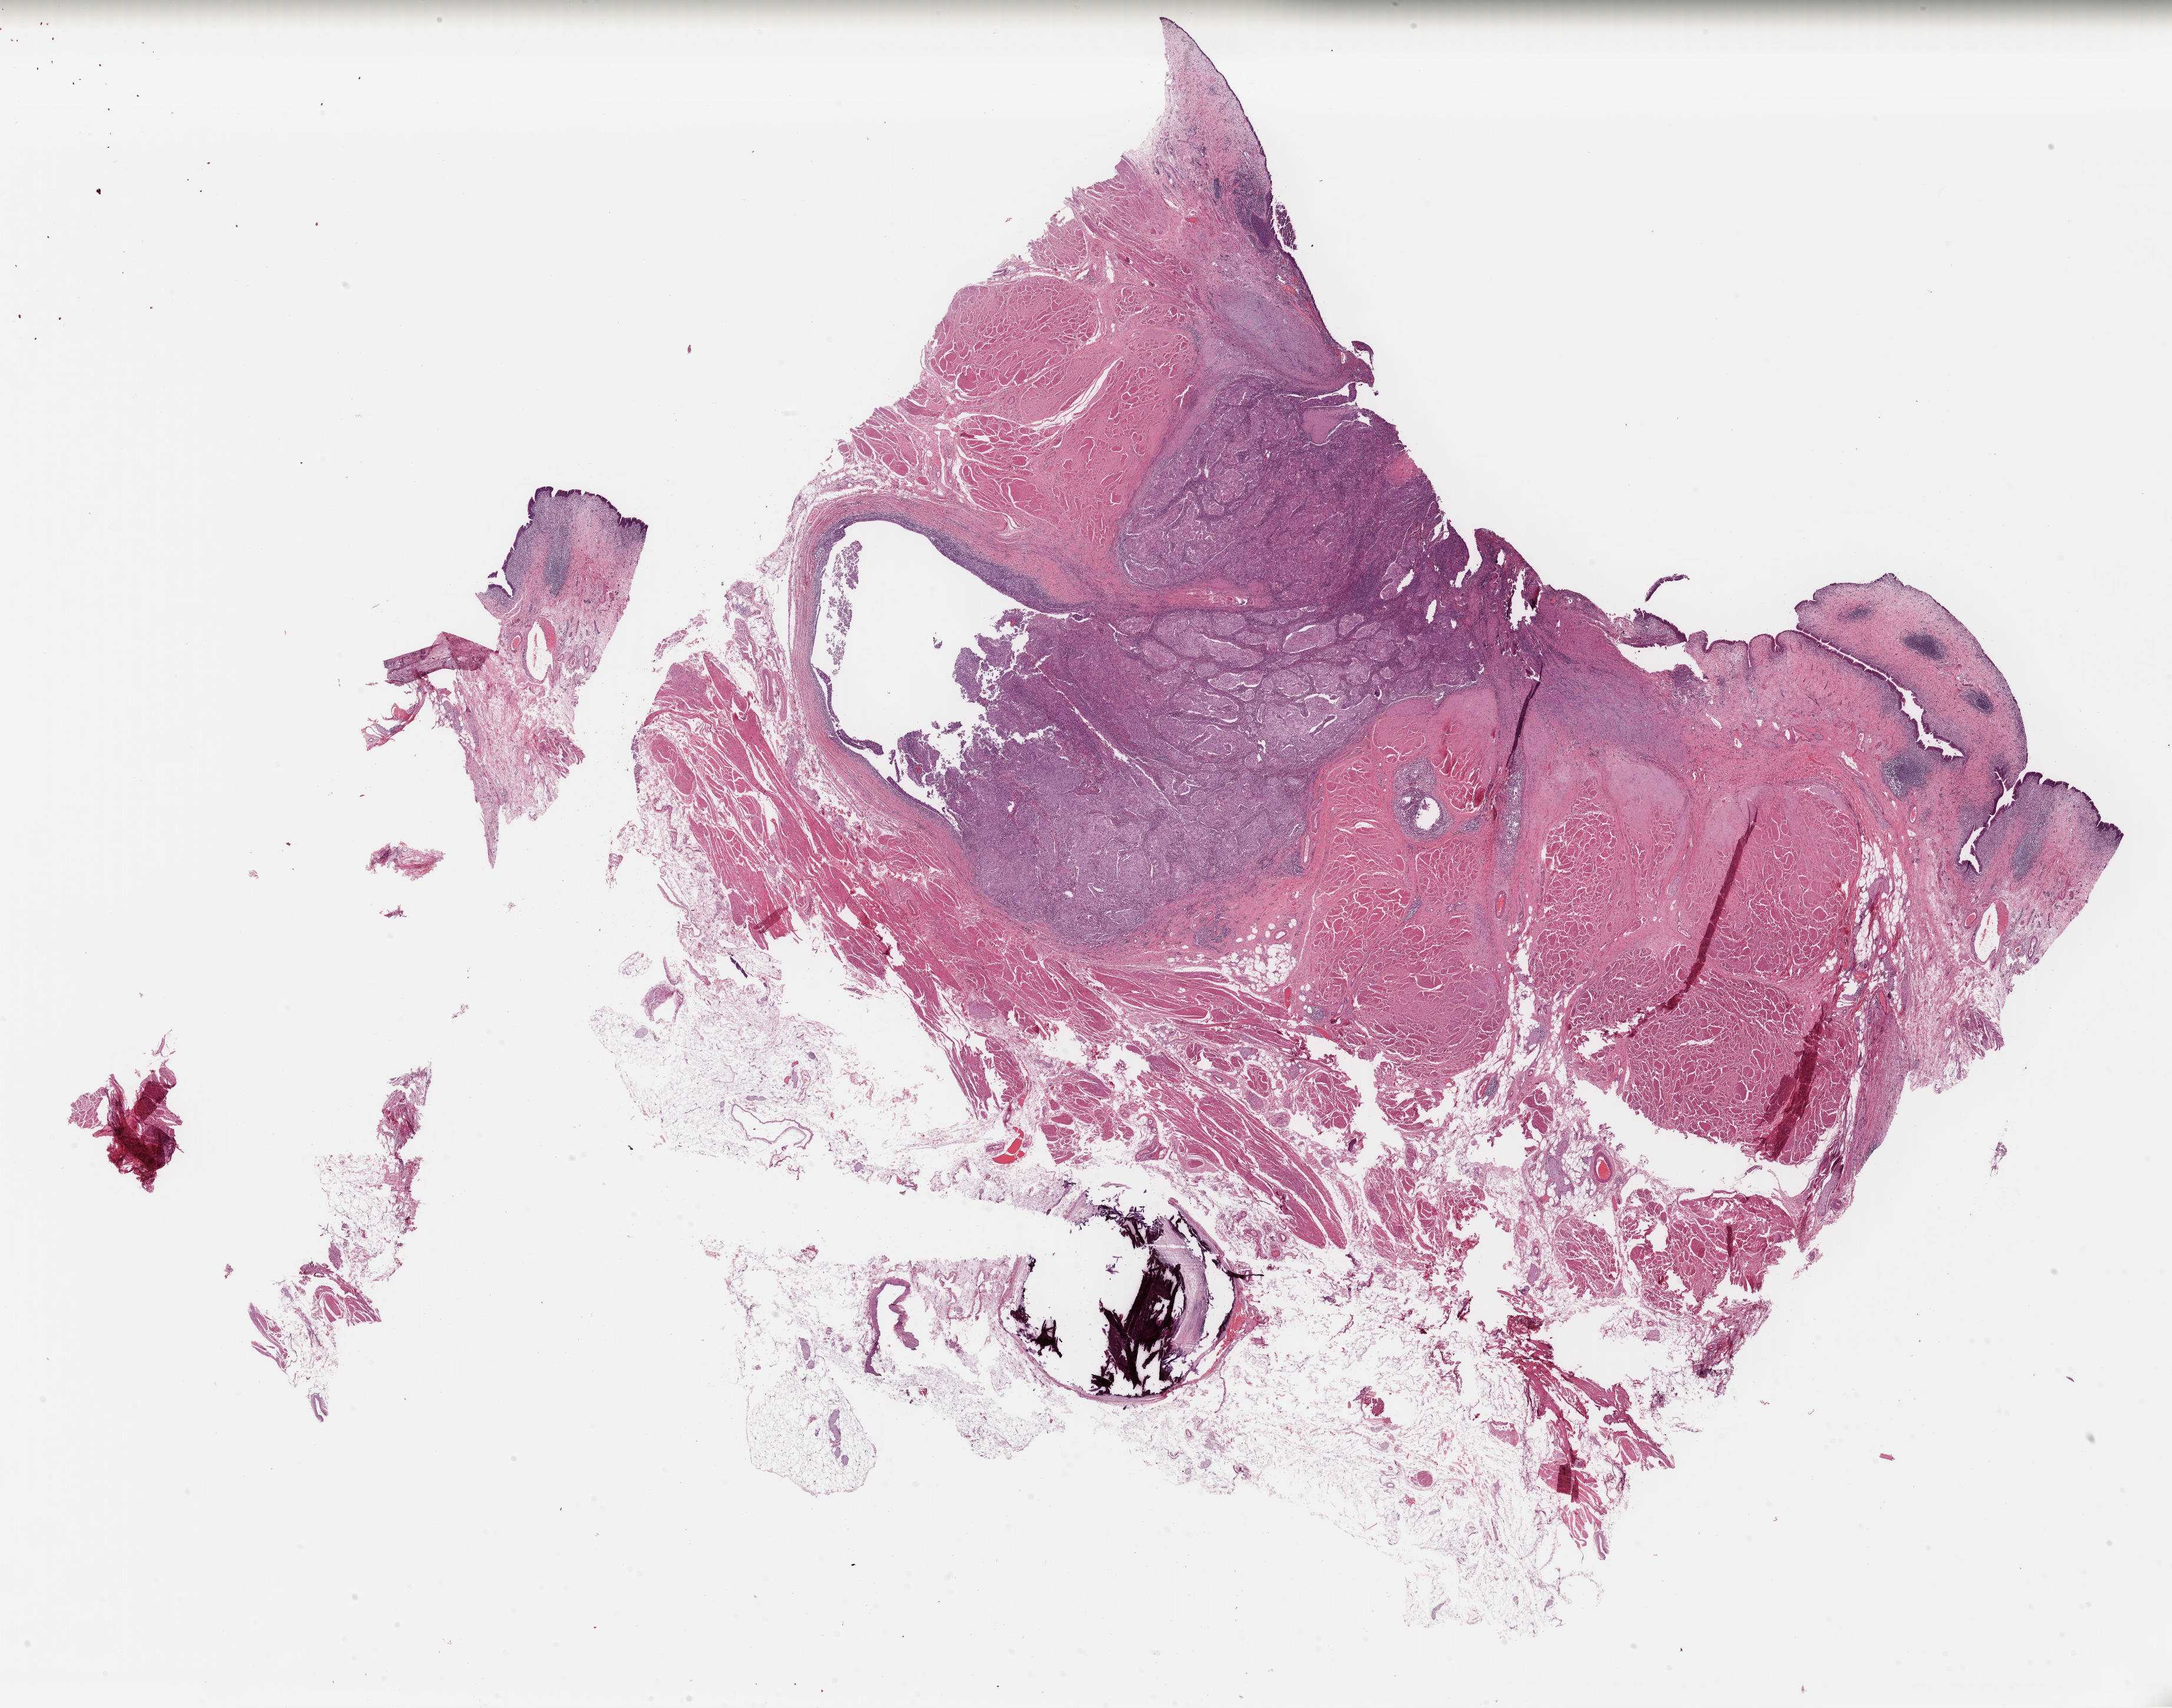
Hematoxylin and eosin (H&E) stained whole-slide image — whole scanned area (about 29.0 x 22.8 mm) shown as a low-resolution overview; FFPE section; bladder, primary tumour sample. Male patient; age at initial diagnosis 64 years. Histologic grade: high grade.
AJCC pathologic stage: IV. Pathologic diagnosis: Transitional cell carcinoma. Lymph nodes positive (case pathology): 1 of 10 examined. TNM: T4a N1 MX.